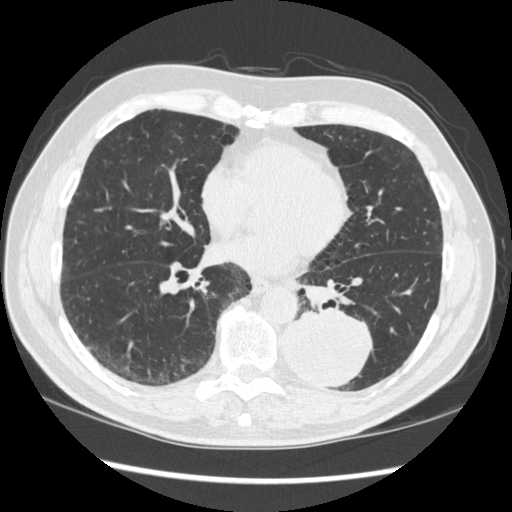
Low-dose screening chest CT, one axial slice. Position 138 of 348 along the scan axis. 120 kVp. Lung window (W 1500 / L -600 HU). 512 × 512 image matrix, field of view 360 × 360 mm.
Annotated regions visible in this slice (expert manual segmentation):
- lesion 1 (tumor, lower lobe of left lung): box from (x=283, y=310) to (x=373, y=387) px